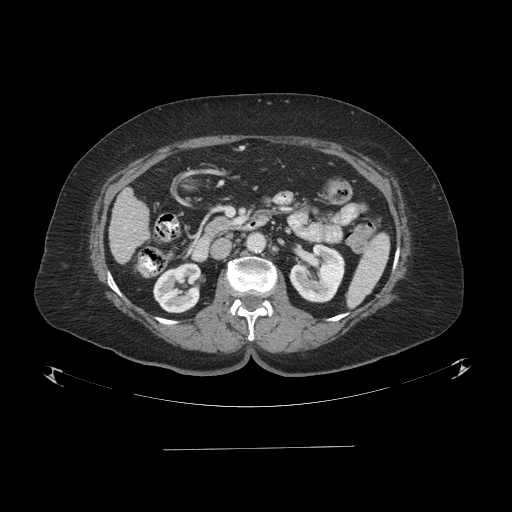
Contrast-enhanced abdominal CT (liver protocol), one axial slice; position 27 of 103 along the scan axis; reconstruction kernel STANDARD; 120 kVp; one of 2 acquisitions stored at this slice position; soft-tissue window (W 400 / L 40 HU); 512 × 512 image matrix, field of view 500 × 500 mm. From the clinical record (not read from this slice): diagnosis: hepatocellular carcinoma (patient treated with transarterial chemoembolisation; whether this scan precedes or follows treatment is not stated here); TNM stage (as recorded): Stage-IIIA; Child-Pugh class: A; tumour differentiation: poorly differentiated.
Outlined on this slice (semi-automatically segmented with operator editing):
- liver parenchyma outside the tumour (the mass and vessels are separate outlines, so this box may not span the whole liver): bounding box <108,188,148,264> (left, top, right, bottom; pixels)